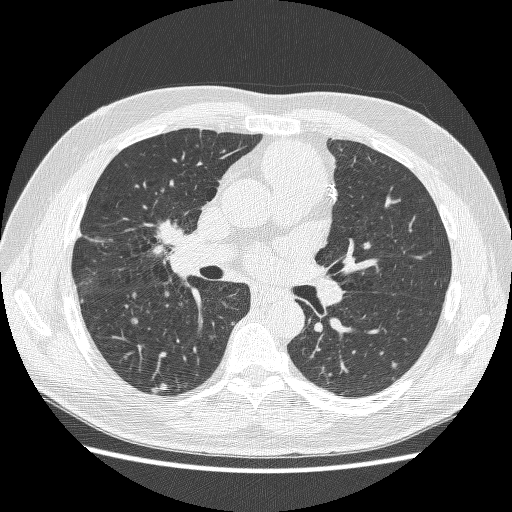
Low-dose screening chest CT, axial slice, first (baseline) screen, lung window (W 1500 / L -600 HU), 1.25 mm slice thickness. Male participant, aged 59 years at enrolment. Former smoker at enrolment.
Expert-annotated lung lesion, bounding box <130,214,199,277> (left, top, right, bottom; pixels). No non-calcified nodule or mass ≥4 mm was recorded by the screening reader at this exam. Lung cancer was diagnosed 24 days after this screen: adenocarcinoma, NOS, right middle lobe, poorly differentiated (G3), stage IV (AJCC 6th edition), 54 mm at pathology.